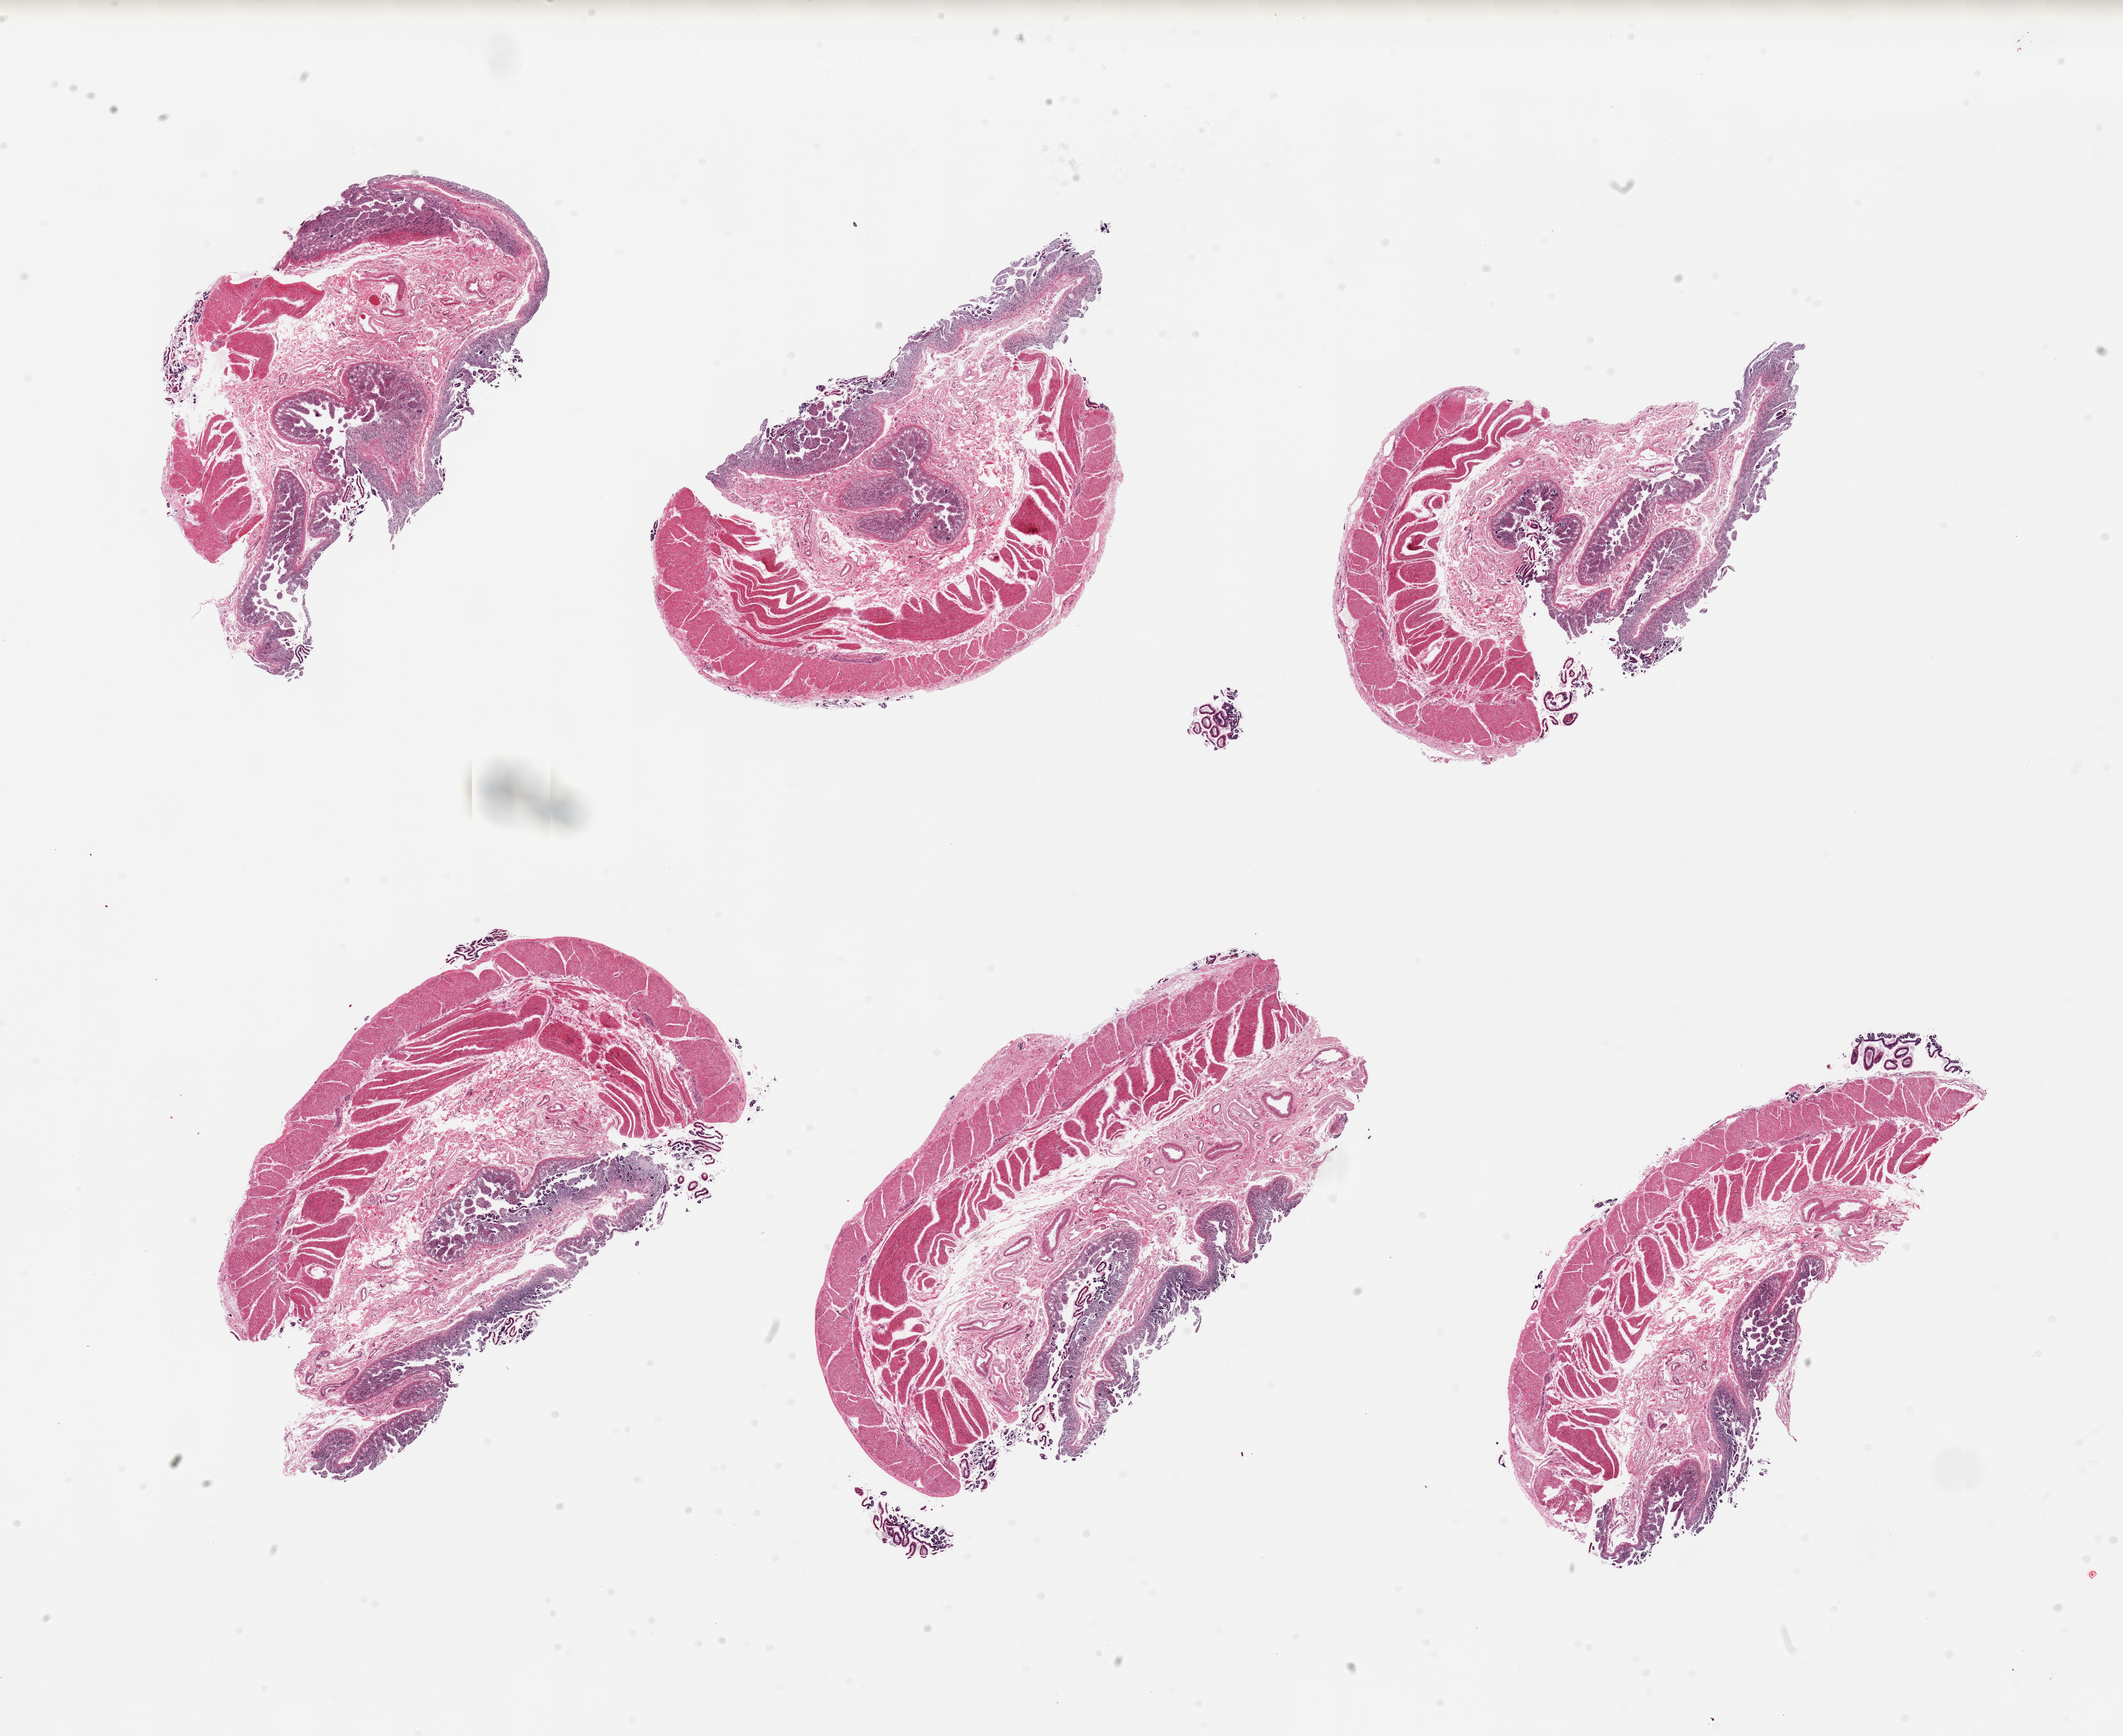
Digitized haematoxylin and eosin-stained section, shown as a low-resolution overview of the whole scanned area (about 26.6 x 21.7 mm). PAXgene-fixed paraffin-embedded (PFPE) section. Target tissue: transverse colon. Tissue donor sample. Donor: female.
- pathologist's review note for this sample: 6 pieces; autolyzed small bowel (not target) mucosa and muscularis